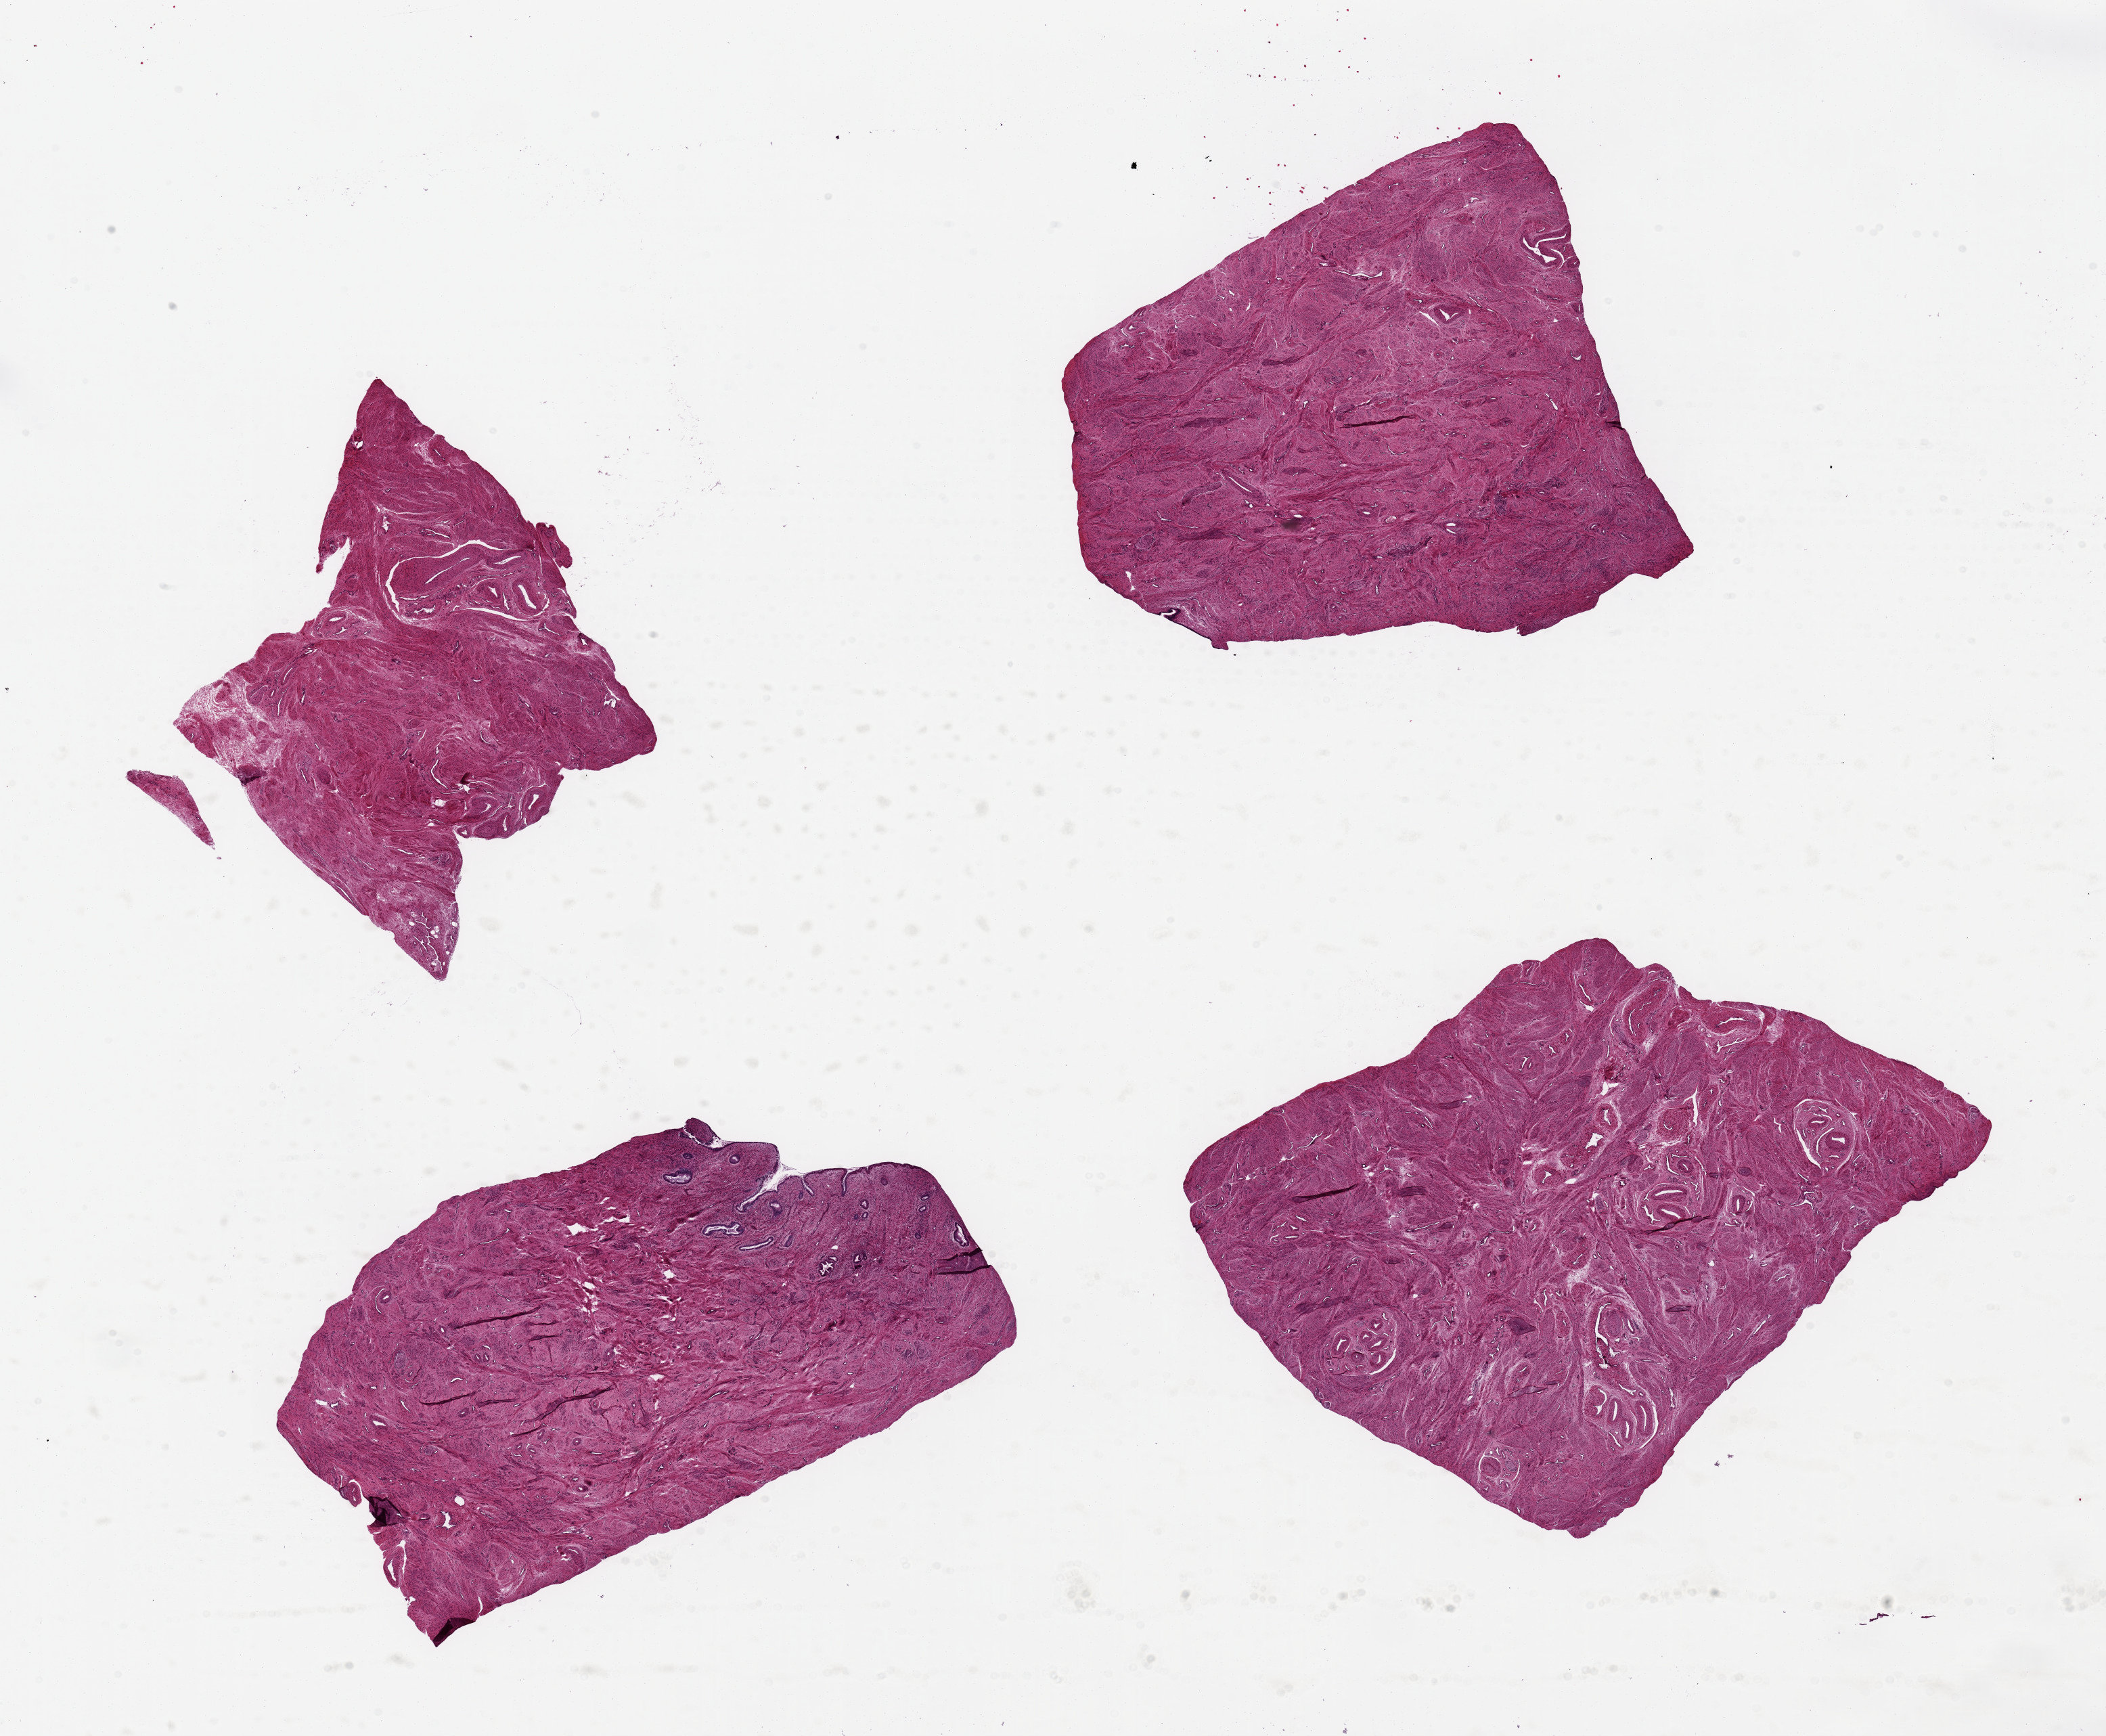
Digitized hematoxylin and eosin (H&E)-stained section — low-resolution overview of the scanned area, about 24.6 x 20.3 mm; PAXgene-fixed paraffin-embedded (PFPE) section; section of endocervix (target tissue); tissue donor sample.
- review note (as recorded): 6 pieces, ~8x5mm, no glands